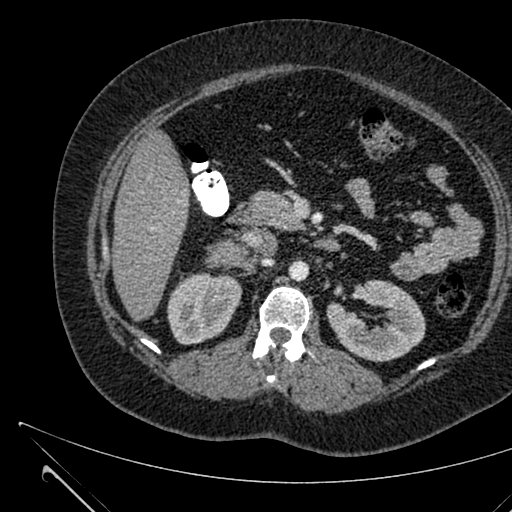
Contrast-enhanced abdominal CT, one axial slice. Position 353 of 731 along the scan axis. Intravenous contrast given. Soft-tissue window (W 400 / L 40 HU). 512 × 512 image matrix, field of view 376 × 376 mm. Female patient, age 36 years. From the clinical record (not read from this slice): diagnosis: adrenocortical carcinoma; tumour side: right adrenal; tumour size at pathology: 10 cm; Ki-67 index: 20 %; stage (as recorded): 4.
Outlined on this slice (semi-automatically segmented with operator editing):
- mass: bounding box [x1, y1, x2, y2] px = [213, 240, 244, 266]